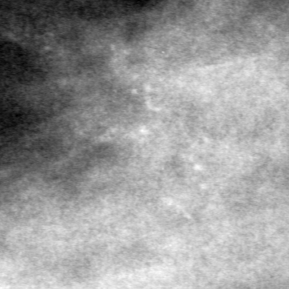
Region of interest cut from a scanned film mammogram (one marked finding); left breast; MLO view.
Calcifications, morphology pleomorphic, distribution clustered; BI-RADS assessment category 4; pathology result (as recorded, not read from the image): malignant.